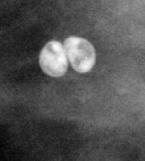
Region of interest cut from a scanned film mammogram (one marked finding); left breast; CC view.
- Marked abnormality: calcifications, morphology lucent center; BI-RADS assessment category 2; subtlety rating 3 on a 1 (subtle) to 5 (obvious) scale; benign without callback (not worked up further).